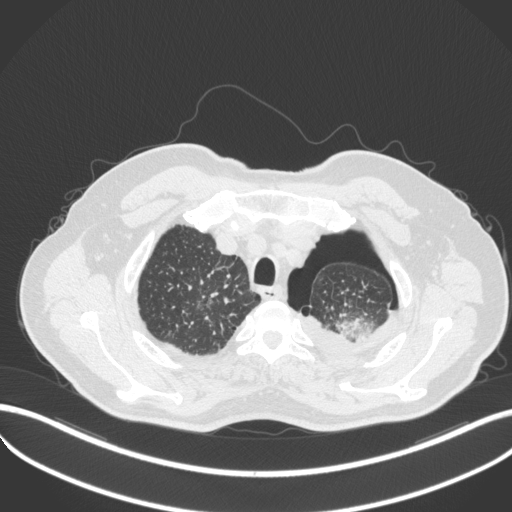
Chest CT, one axial slice. Slice 424 of 466 in the series (ordered by position). Reconstruction kernel B31f. Lung window (W 1500 / L -600 HU). 1 mm slice thickness. 512 × 512 image matrix, field of view 400 × 400 mm. Male patient, age 76 years. From the clinical record (not read from this slice): clinical TNM (as recorded): T3 N0 M1b.
Structures marked on this image (bounding box drawn by a radiologist):
- lung tumour (recorded histology: adenocarcinoma): bounding box (x1, y1, x2, y2) in pixels: (337, 315, 374, 341)